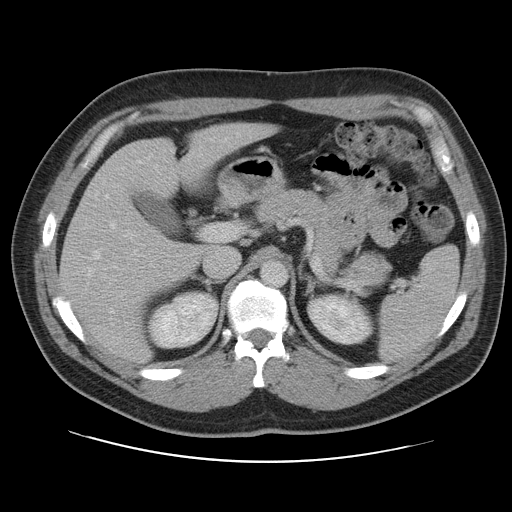
Contrast-enhanced abdominal CT, one axial slice; position 68 of 109 along the scan axis; 120 kVp; intravenous contrast given; soft-tissue window (W 400 / L 40 HU); 512 × 512 image matrix, field of view 402 × 402 mm. Male patient, age 35 years. From the clinical record (not read from this slice): diagnosis: colorectal cancer liver metastases, imaged before liver resection; multiple liver metastases: yes; largest metastasis: 2.8 cm; disease in both lobes: yes.
Outlined on this slice (expert manual segmentation):
- hepatic veins: bounding box (x1, y1, x2, y2) in pixels: (86, 139, 226, 314)
- liver: (60, 125, 271, 361)
- planned liver remnant (the part of the liver to remain after resection): (60, 125, 272, 362)
- portal vein (with intrahepatic branches): (86, 226, 208, 285)